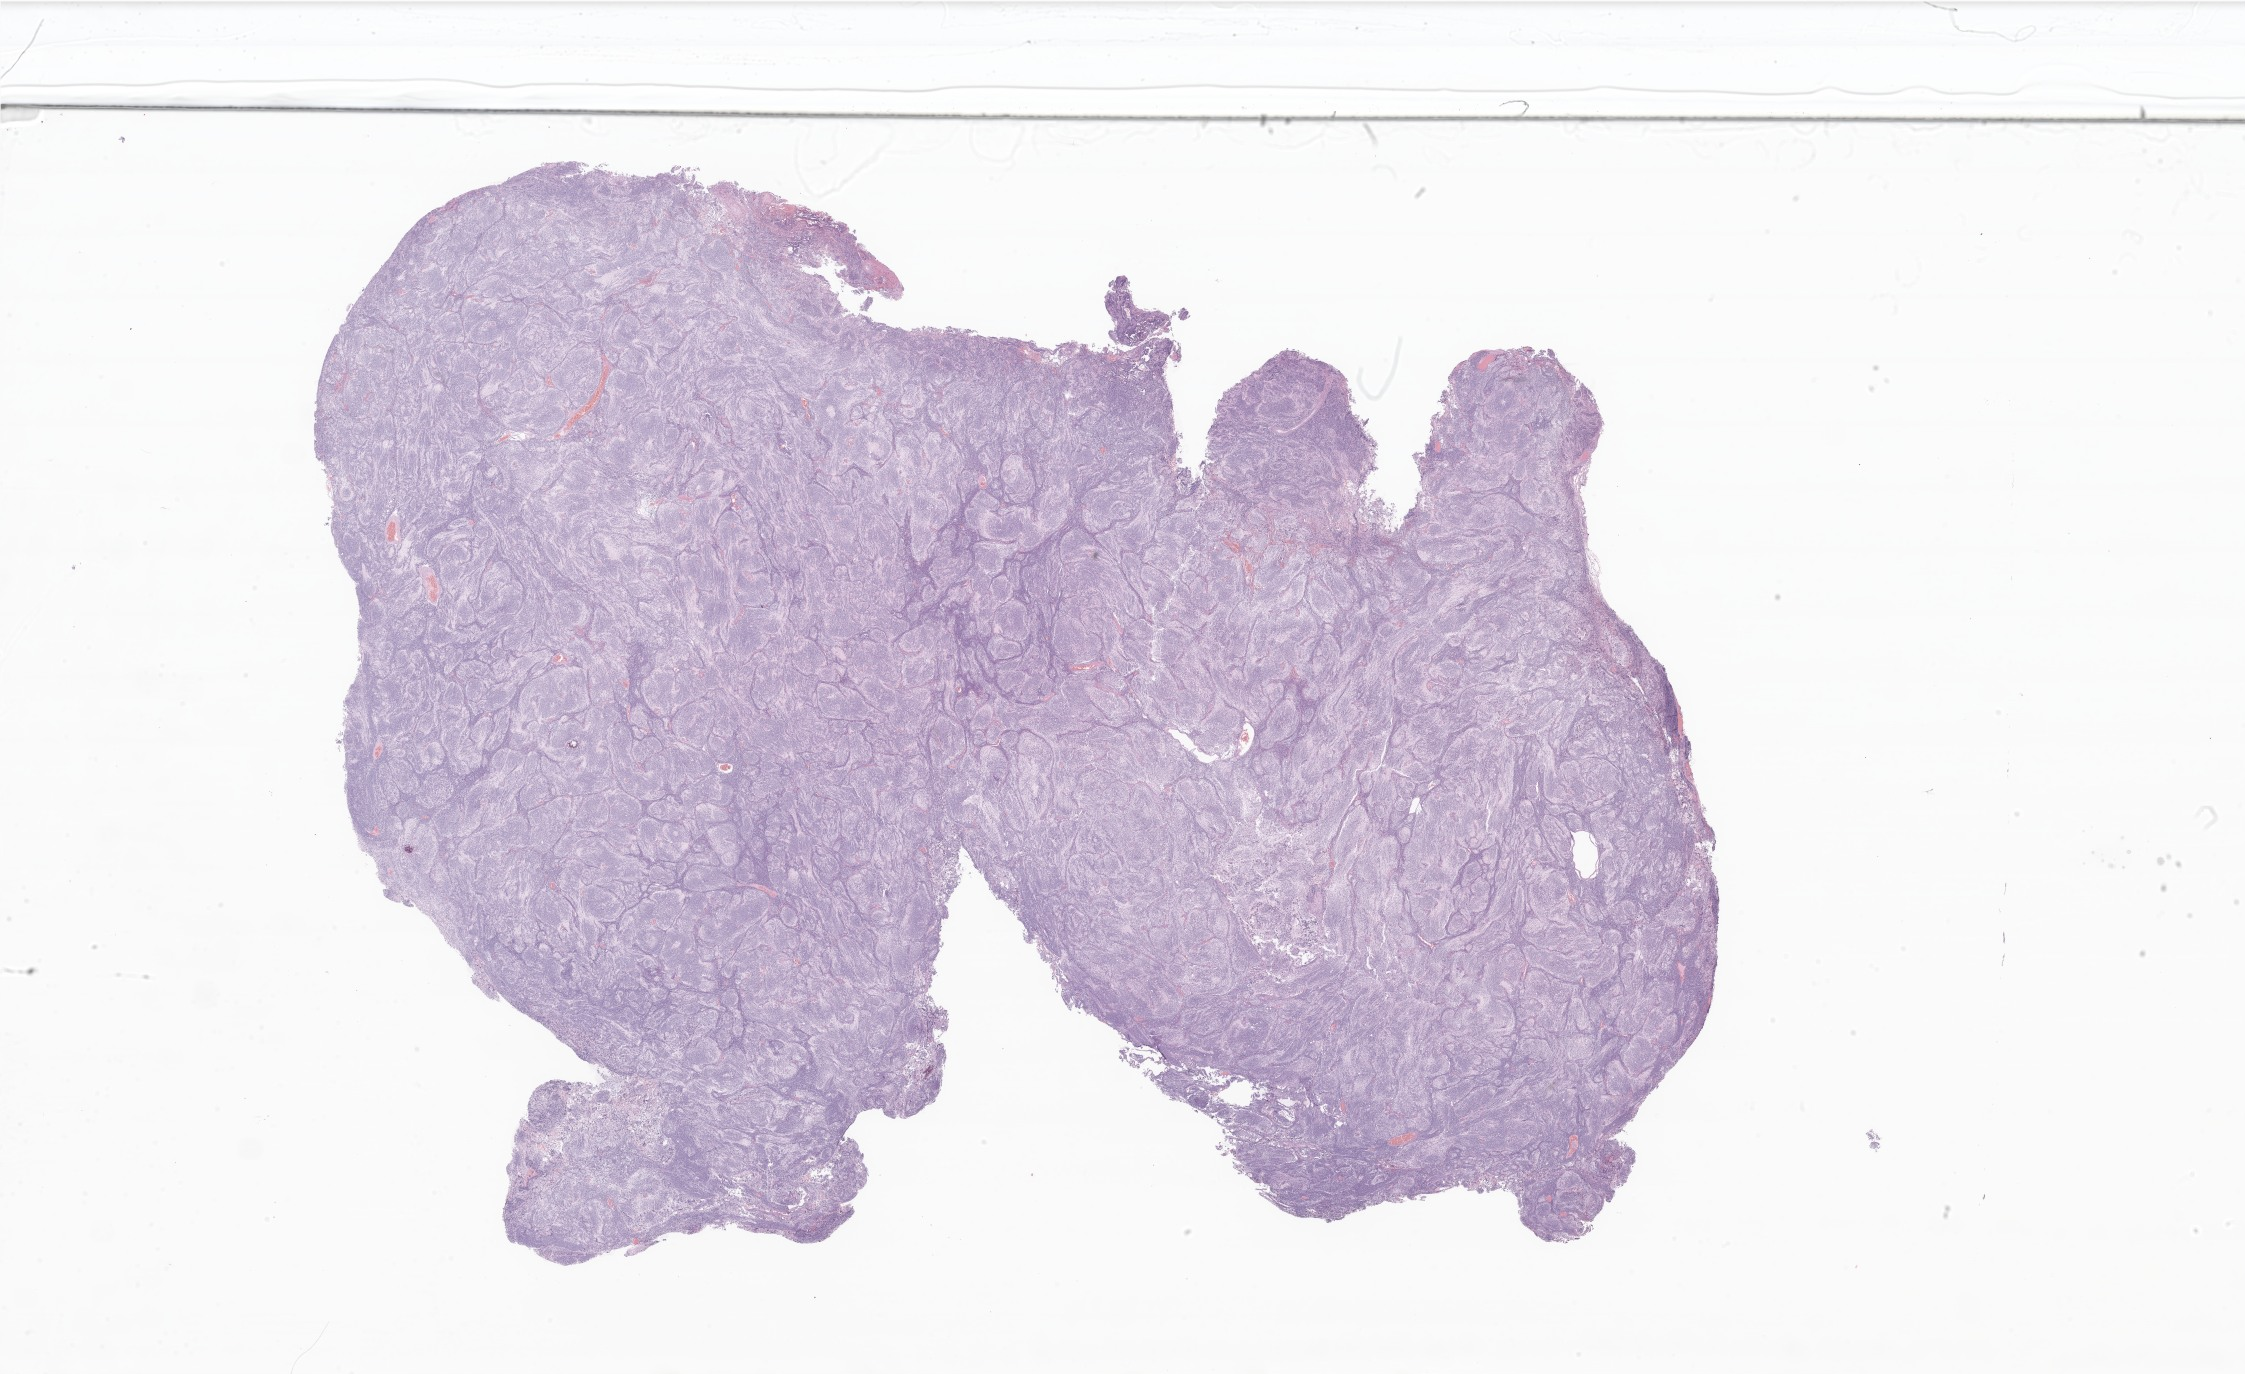
Haematoxylin and eosin whole-slide image of tumor tissue from the brain — low-resolution overview of the scanned area, about 37.9 x 23.2 mm, formalin-fixed, paraffin-embedded (FFPE) tissue. Female patient, age 620 days (about 1.7 years).
- diagnosis (ICD-O-3 morphology term): Medulloblastoma, NOS